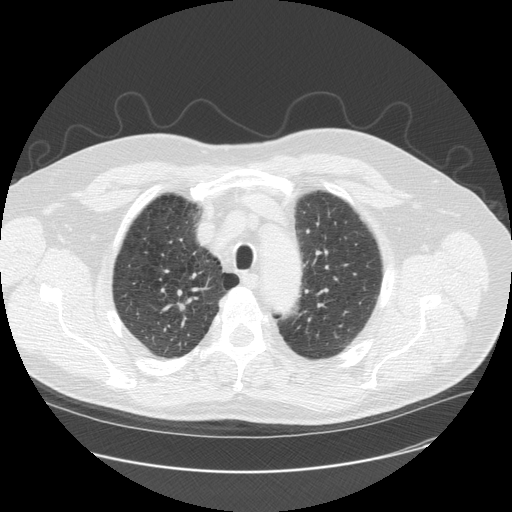
Chest CT (low-dose screening protocol), one axial image. Second annual screen. Lung window (W 1500 / L -600 HU). 2.5 mm slice thickness. 120 kVp. Slice 36 of 179 in the series. Male, age 61 years at enrolment. Former smoker at enrolment.
Expert reader's lesion annotation, box from (x=158, y=286) to (x=204, y=330) px. Screening reader's record for this exam: no non-calcified nodule ≥4 mm recorded. Official screen result: negative screen, minor abnormalities not suspicious for lung cancer. Participant outcome: lung cancer diagnosed 467 days after this screen — squamous cell carcinoma, NOS, right upper lobe, moderately differentiated (G2), stage IA (AJCC 6th edition), 10 mm at pathology.